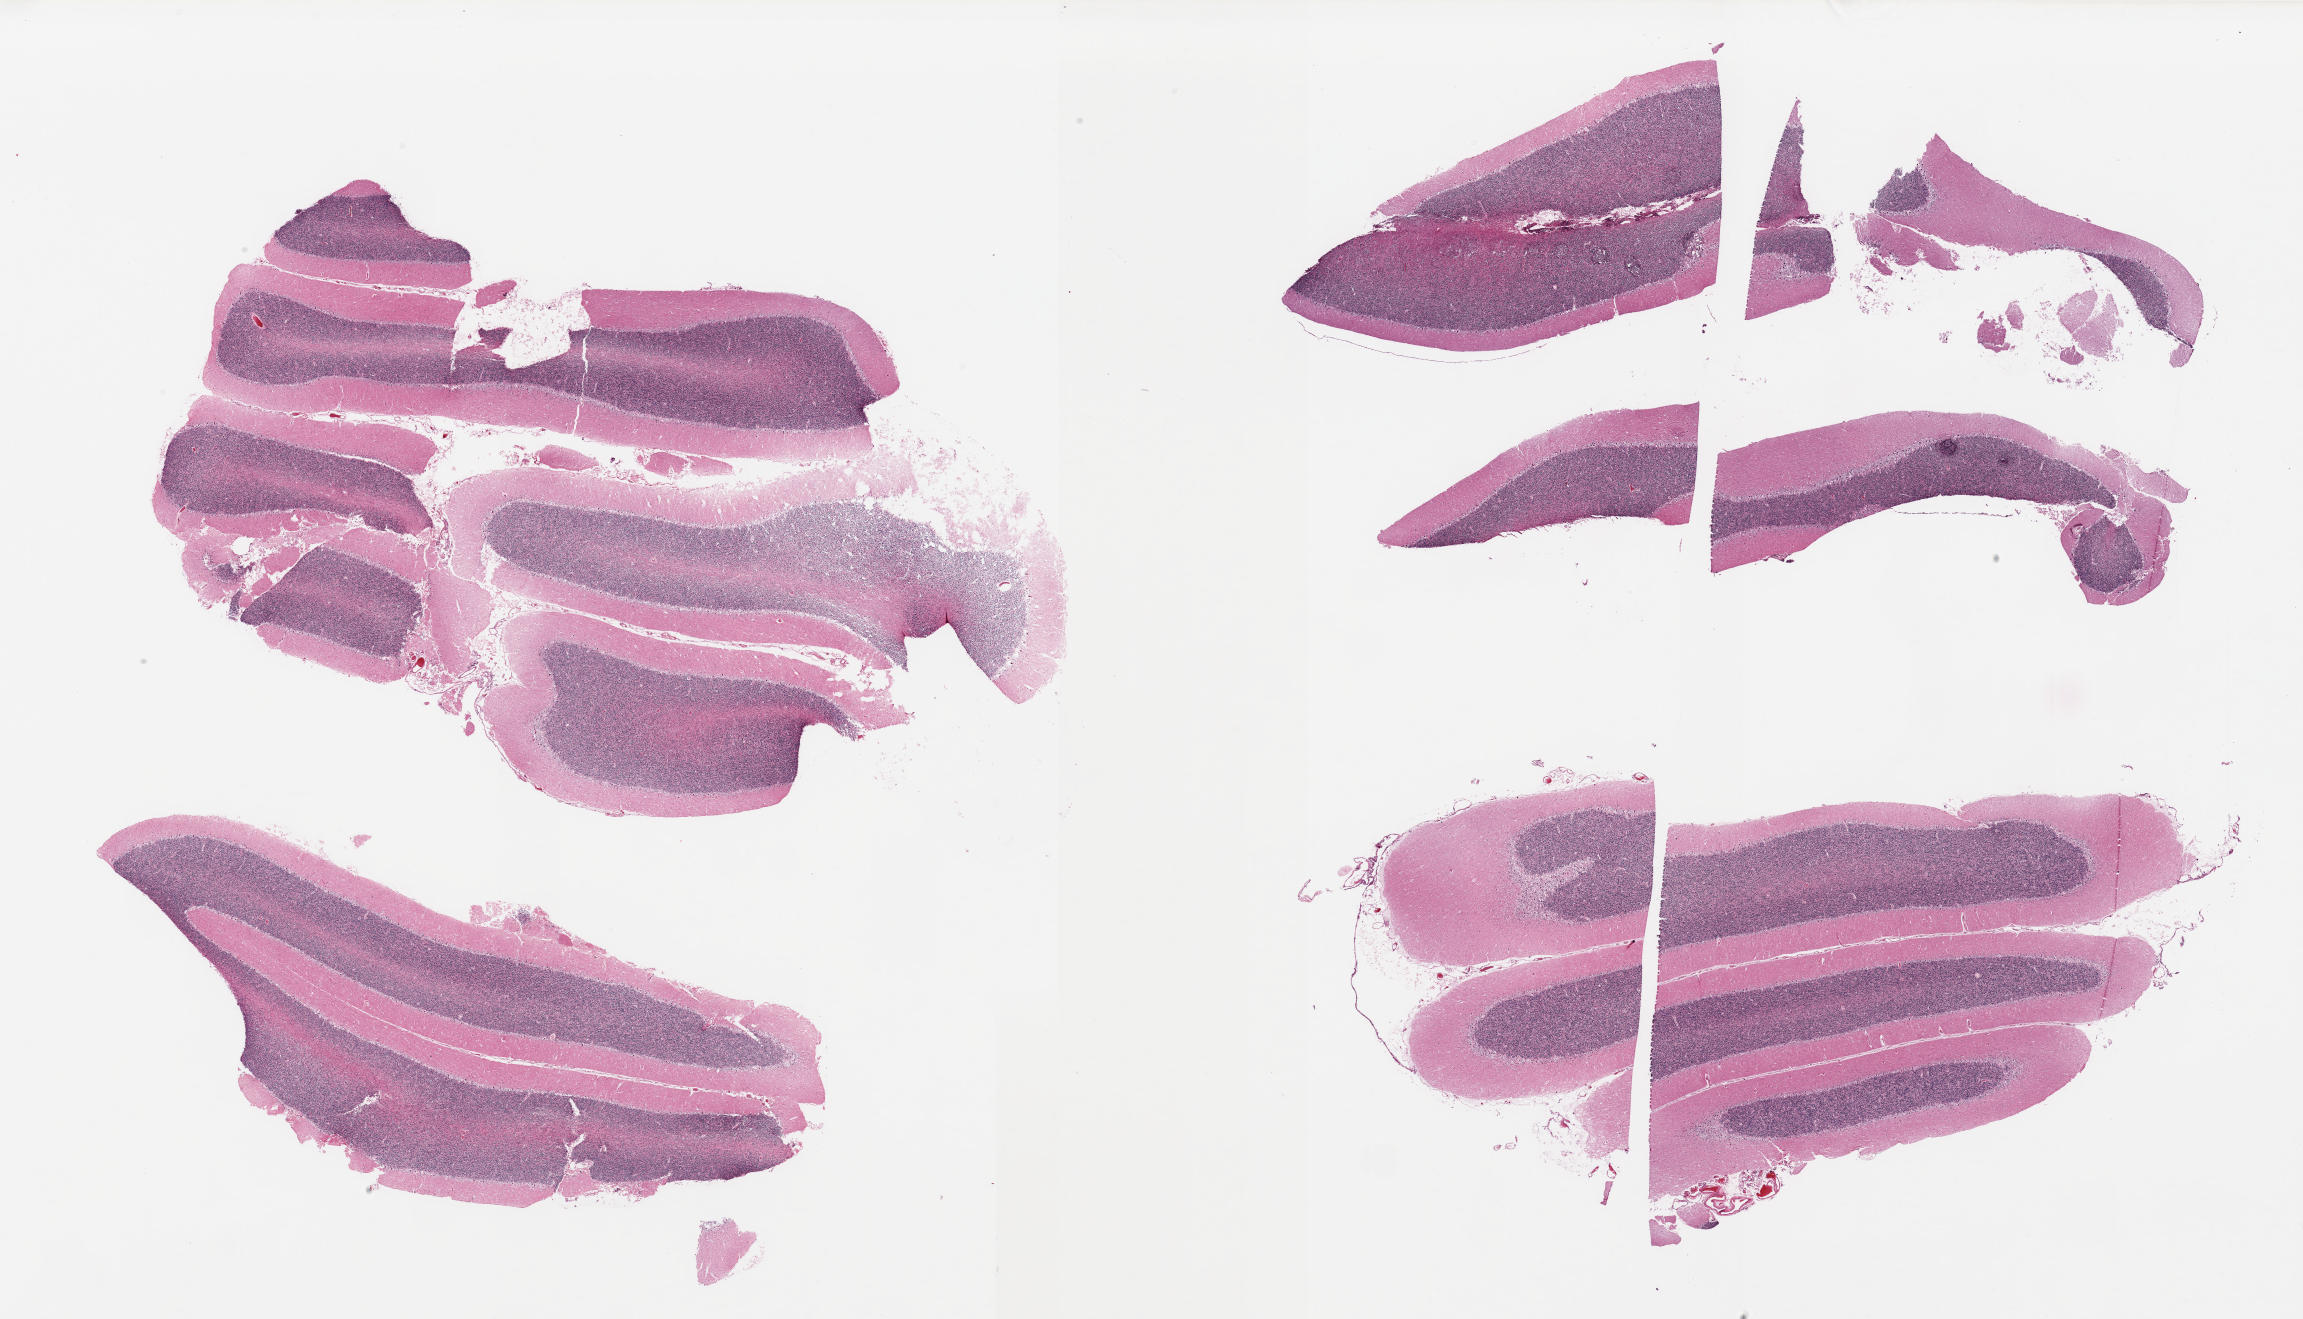
Whole-slide image, haematoxylin and eosin stain, low-resolution overview of the scanned area, about 36.4 x 20.9 mm; PAXgene-fixed, paraffin-embedded tissue; sampled site (target tissue): cerebellum; tissue donor sample. Donor: male.
- reviewer comment on this tissue sample: 4 pieces (fragmented); no abnormalities